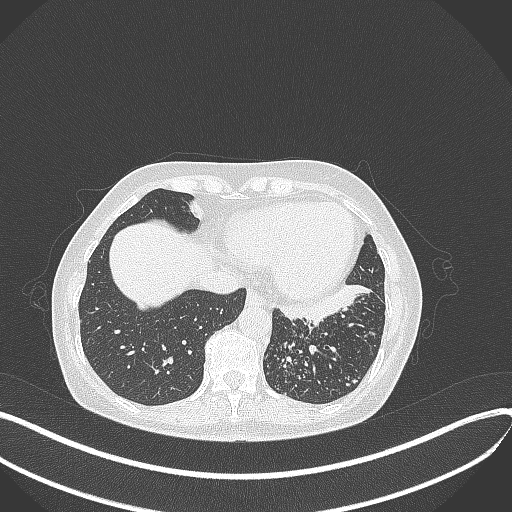
Chest CT, one axial slice. Position 110 of 429 along the scan axis. Reconstruction kernel B70f. 100 kVp. Lung window (W 1500 / L -600 HU). 1 mm slice thickness. 512 × 512 image matrix, field of view 400 × 400 mm. Female patient, age 63 years. From the clinical record (not read from this slice): clinical TNM (as recorded): T1b N0 M0; histopathological grade: G2-3.
Structures marked on this image (rectangle marked by the reading radiologist):
- lung tumour (recorded histology: adenocarcinoma): bounding box [x1, y1, x2, y2] px = [275, 282, 375, 323]